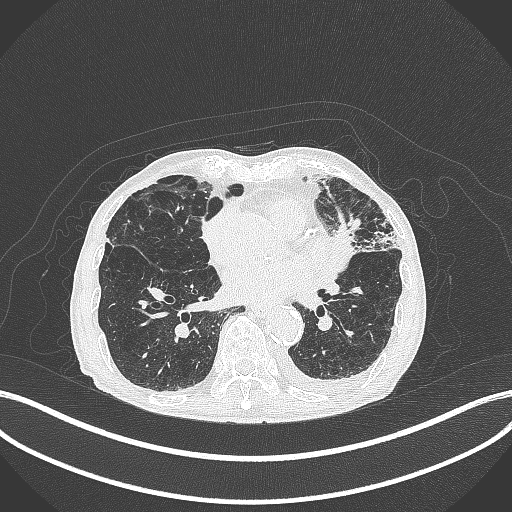
Chest CT, one axial slice; position 156 of 385 along the scan axis; 120 kVp; lung window (W 1500 / L -600 HU); 1 mm slice thickness; 512 × 512 image matrix, field of view 400 × 400 mm. Male patient, age 90 years or older. From the clinical record (not read from this slice): clinical TNM (as recorded): T2b N1 M0.
Structures marked on this image (rectangle marked by the reading radiologist):
- lung tumour (recorded histology: squamous cell carcinoma): bounding box (x1, y1, x2, y2) in pixels: (330, 217, 358, 273)